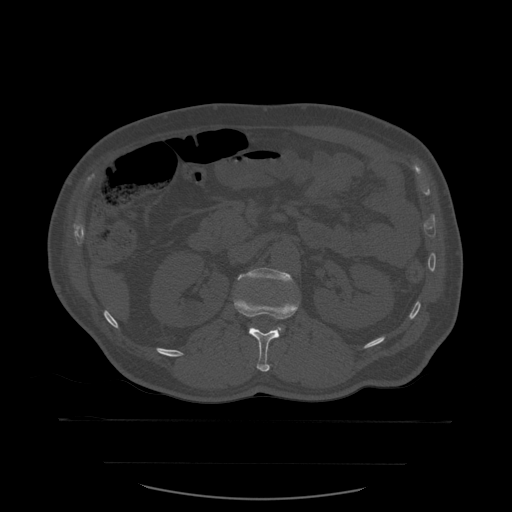
CT including the spine, one axial slice. Slice 239 of 590 in the series (ordered by position). Bone window (W 1800 / L 400 HU). 1.25 mm slice thickness. 512 × 512 image matrix, field of view 479 × 479 mm. Patient age 71 years. From the clinical record (not read from this slice): primary cancer: lung; vertebrae with lytic lesions (as recorded): T1, T2, L5, S1.
Annotated regions visible in this slice (semi-automatic segmentation, software-assisted and operator-edited):
- L1 vertebra: bounding box <234,280,300,372> (left, top, right, bottom; pixels)
- L2 vertebra: <238,268,294,335>